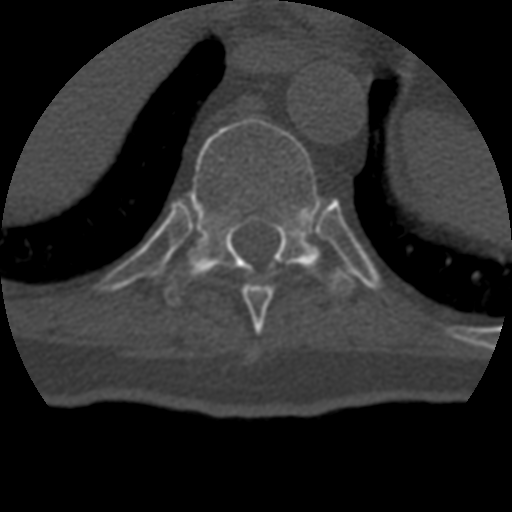
CT including the spine, one axial slice. Position 227 of 399 along the scan axis. Reconstruction kernel STANDARD. Bone window (W 1800 / L 400 HU). 1.25 mm slice thickness. 512 × 512 image matrix, field of view 160 × 160 mm. Patient age 69 years. From the clinical record (not read from this slice): primary cancer: prostate.
Outlined on this slice (semi-automatically segmented with operator editing):
- T10 vertebra: box from (x=165, y=118) to (x=355, y=306) px
- T9 vertebra: (x=219, y=265)–(x=274, y=327)